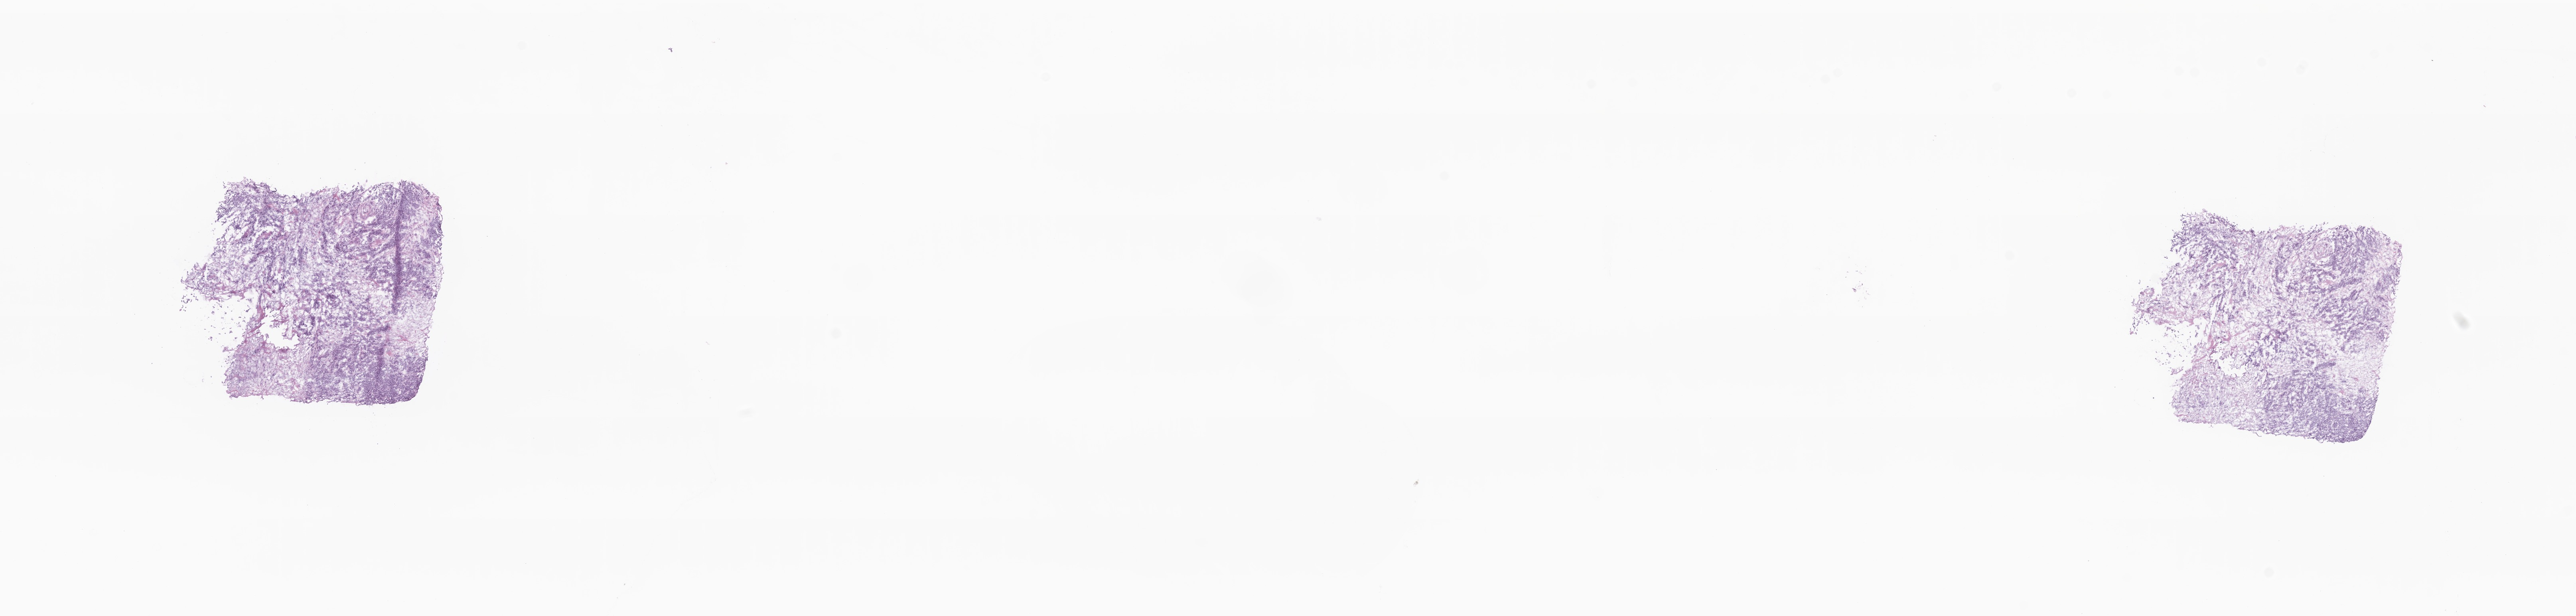
Haematoxylin and eosin whole-slide image — whole scanned area (about 27.2 x 6.5 mm) shown as a low-resolution overview; frozen section (tissue freezing medium); specimen: primary tumor; anatomic site: breast (right). Female patient; age at initial diagnosis 79 years. Composition of this section per pathologist review: tumor cells 100%, tumor nuclei 80%, stromal cells 0%, necrosis 0%, normal cells 0%. Inflammatory infiltration, as recorded: lymphocyte infiltration 0%, monocyte infiltration 0%, neutrophil infiltration 0%.
* section: top of the tissue portion
* histologic diagnosis: Lobular carcinoma, NOS